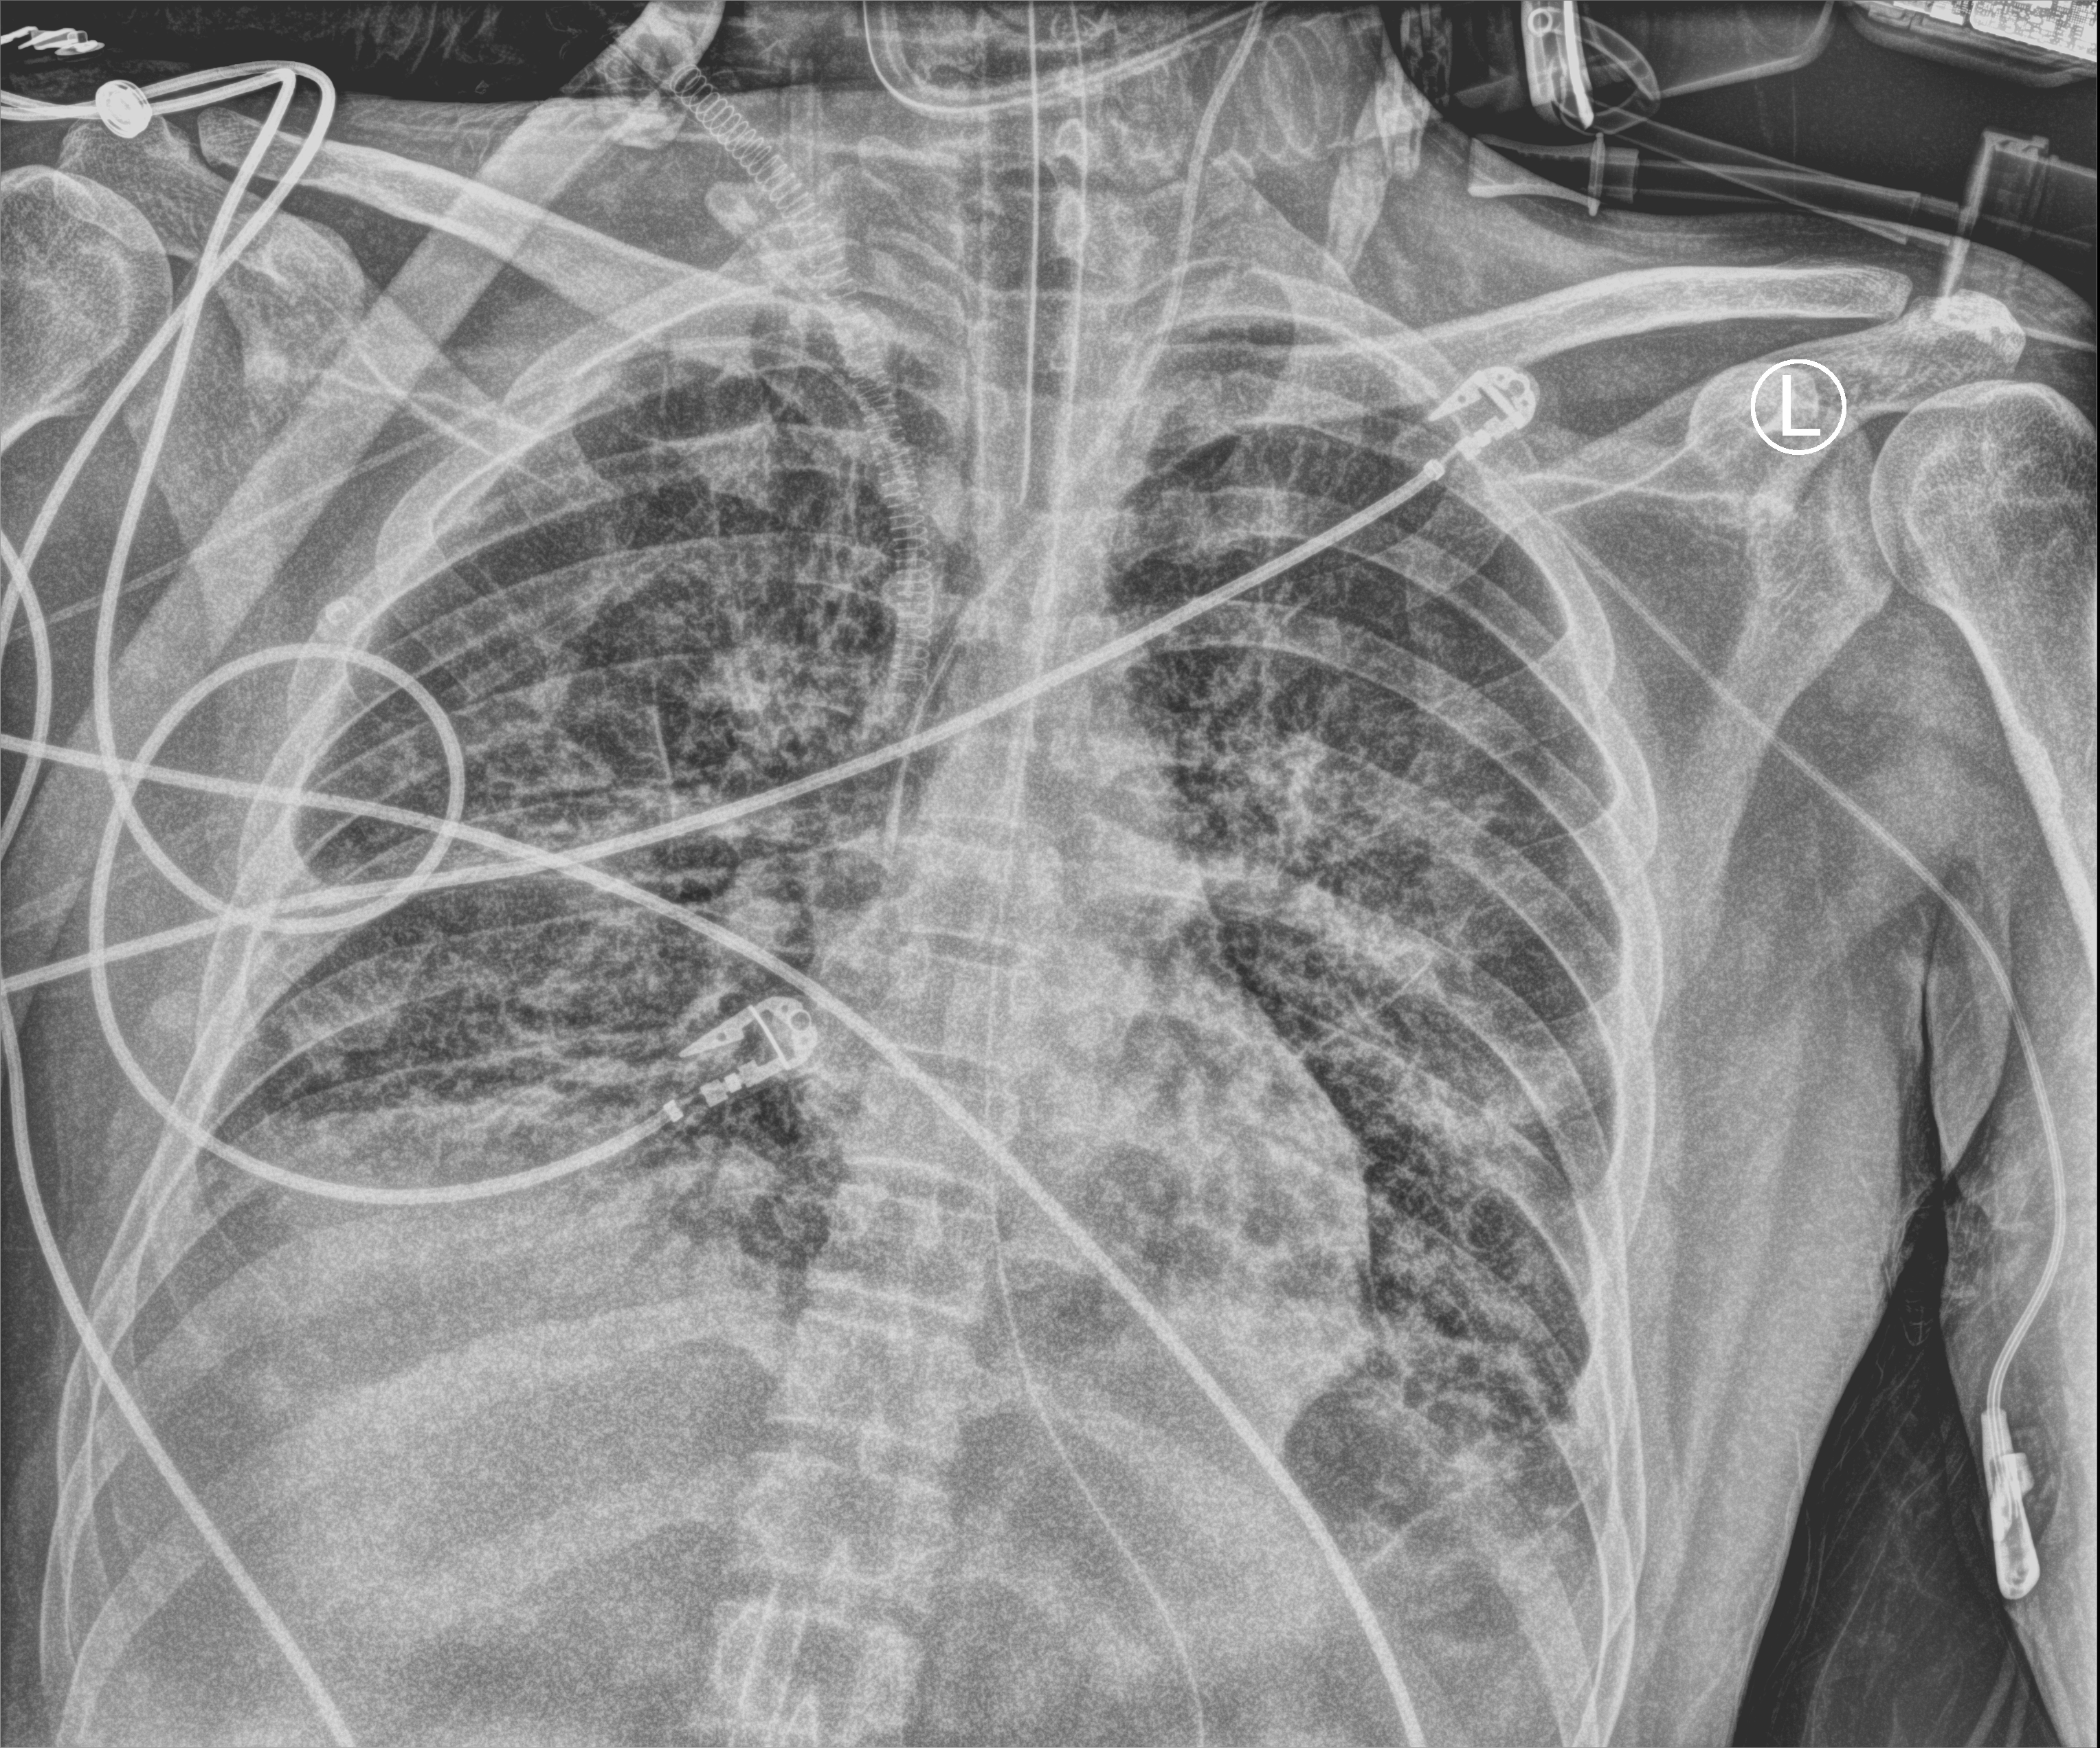
Bedside chest radiograph (computed radiography), anteroposterior (AP) projection. Patient hospitalised with COVID-19, aged 18–59 years.
From the hospital-stay record, not from the radiograph (when in the stay this image was taken is not recorded):
- mechanically ventilated during this hospital stay: yes
- length of hospital stay: 60 days